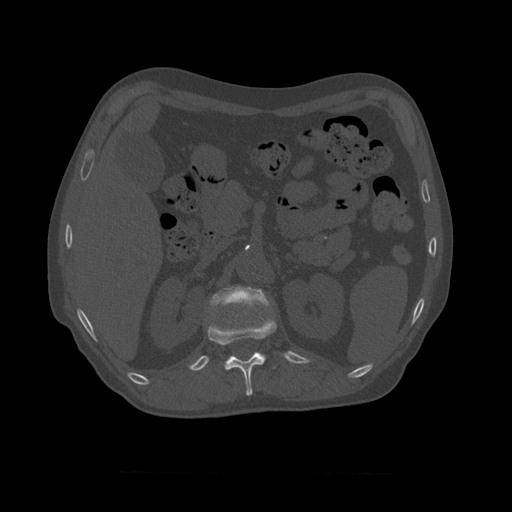
CT including the spine, one axial slice. Position 373 of 450 along the scan axis. Reconstruction kernel STANDARD. Bone window (W 1800 / L 400 HU). 1.25 mm slice thickness. 512 × 512 image matrix, field of view 405 × 405 mm. Patient age 75 years. From the clinical record (not read from this slice): primary cancer: prostate.
Annotated regions visible in this slice (semi-automatically segmented with operator editing):
- L1 vertebra: bounding box (x1, y1, x2, y2) in pixels: (209, 286, 271, 310)
- T11 vertebra: (207, 317, 277, 396)